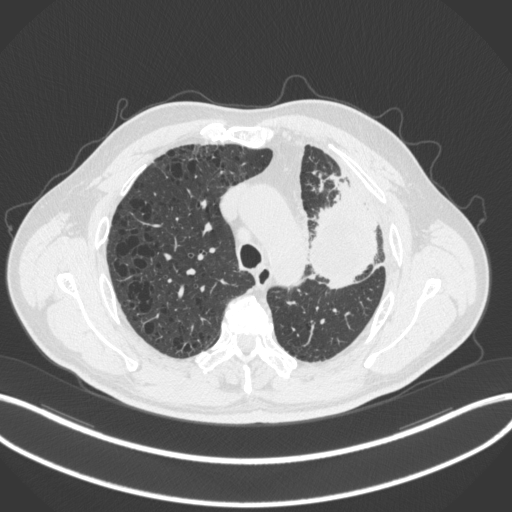
Chest CT, one axial slice; position 218 of 286 along the scan axis; reconstruction kernel B31f; 120 kVp; lung window (W 1500 / L -600 HU); 1 mm slice thickness; 512 × 512 image matrix, field of view 400 × 400 mm. Patient: male, 68 years. From the clinical record (not read from this slice): clinical TNM (as recorded): T3 N3 M1.
Annotated regions visible in this slice (rectangle marked by the reading radiologist):
- lung tumour (recorded histology: adenocarcinoma): box from (x=306, y=171) to (x=377, y=293) px